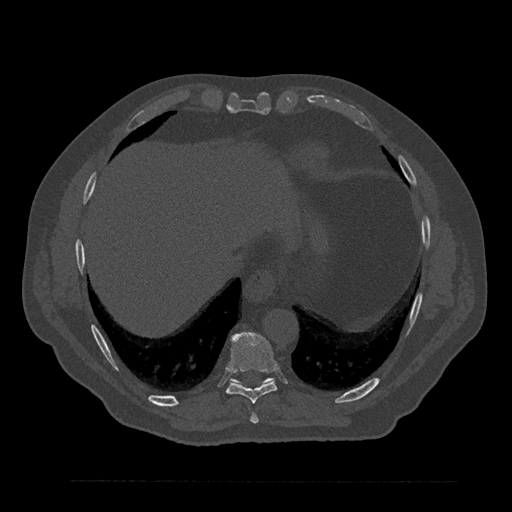
CT including the spine, one axial slice; slice 395 of 797 in the series (ordered by position); reconstruction kernel Br40s/3; 120 kVp; bone window (W 1800 / L 400 HU); 512 × 512 image matrix, field of view 430 × 430 mm. Male patient, age 61 years. Case-level facts recorded for this patient, not image findings: primary cancer: prostate.
Outlined on this slice (semi-automatic segmentation, software-assisted and operator-edited):
- T10 vertebra: bounding box [x1, y1, x2, y2] px = [231, 378, 273, 385]
- T8 vertebra: [250, 413, 259, 424]
- T9 vertebra: [226, 333, 277, 404]